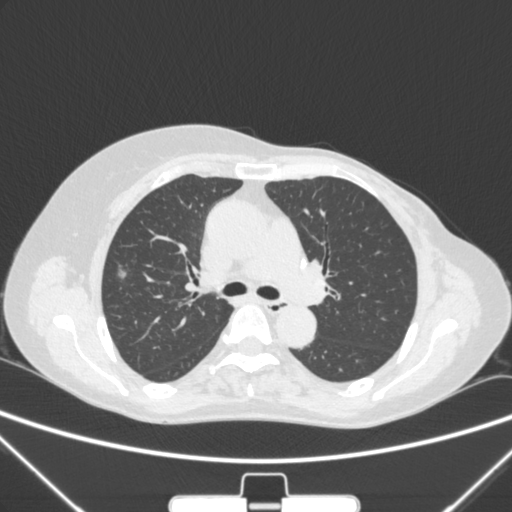
Chest CT, one axial slice; lung window (W 1500 / L -600 HU); 1 mm slice thickness; 512 × 512 image matrix, field of view 350 × 350 mm. Patient: female, 64 years. Case-level facts recorded for this patient, not image findings: clinical TNM (as recorded): T1c N0 M0.
Outlined on this slice (bounding box drawn by a radiologist):
- lung tumour (recorded histology: adenocarcinoma): bounding box [x1, y1, x2, y2] px = [104, 251, 133, 286]